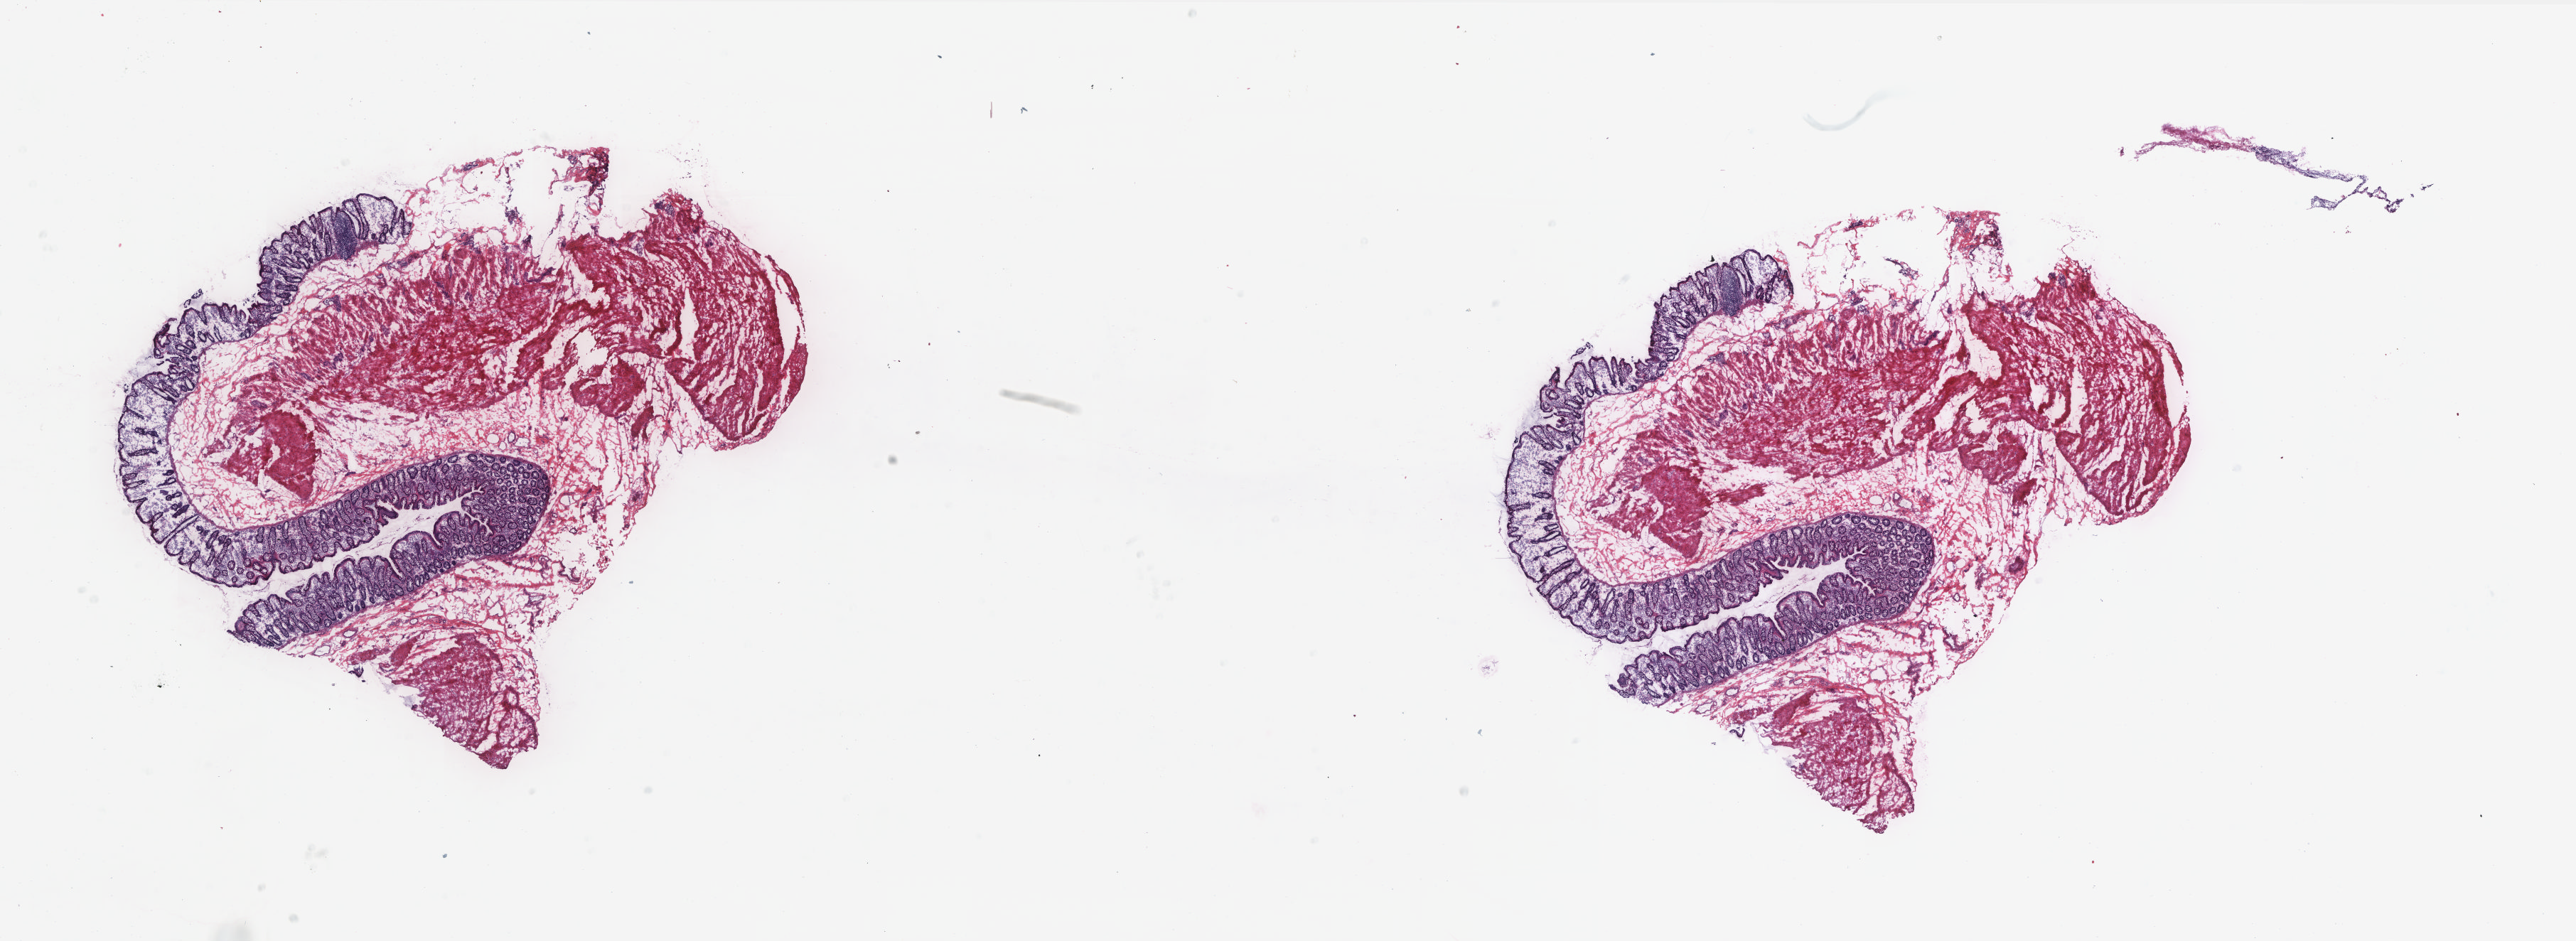
Hematoxylin and eosin (H&E) stained whole-slide image, shown as a low-resolution overview of the whole scanned area (about 28.9 x 10.6 mm, acquisition: 20x scan), frozen section from the bottom of the tissue portion, solid tissue normal (non-tumour tissue) sample from the rectum. Male, age 71 years at initial diagnosis. Slide review estimates, as recorded: tumour cells 0%, normal cells 100%. Infiltration values recorded for this section: lymphocyte infiltration 35%, monocyte infiltration 6%, neutrophil infiltration 3%.
This section: solid tissue normal (non-tumour) sample from the same patient. Patient diagnosis: Adenocarcinoma, NOS.